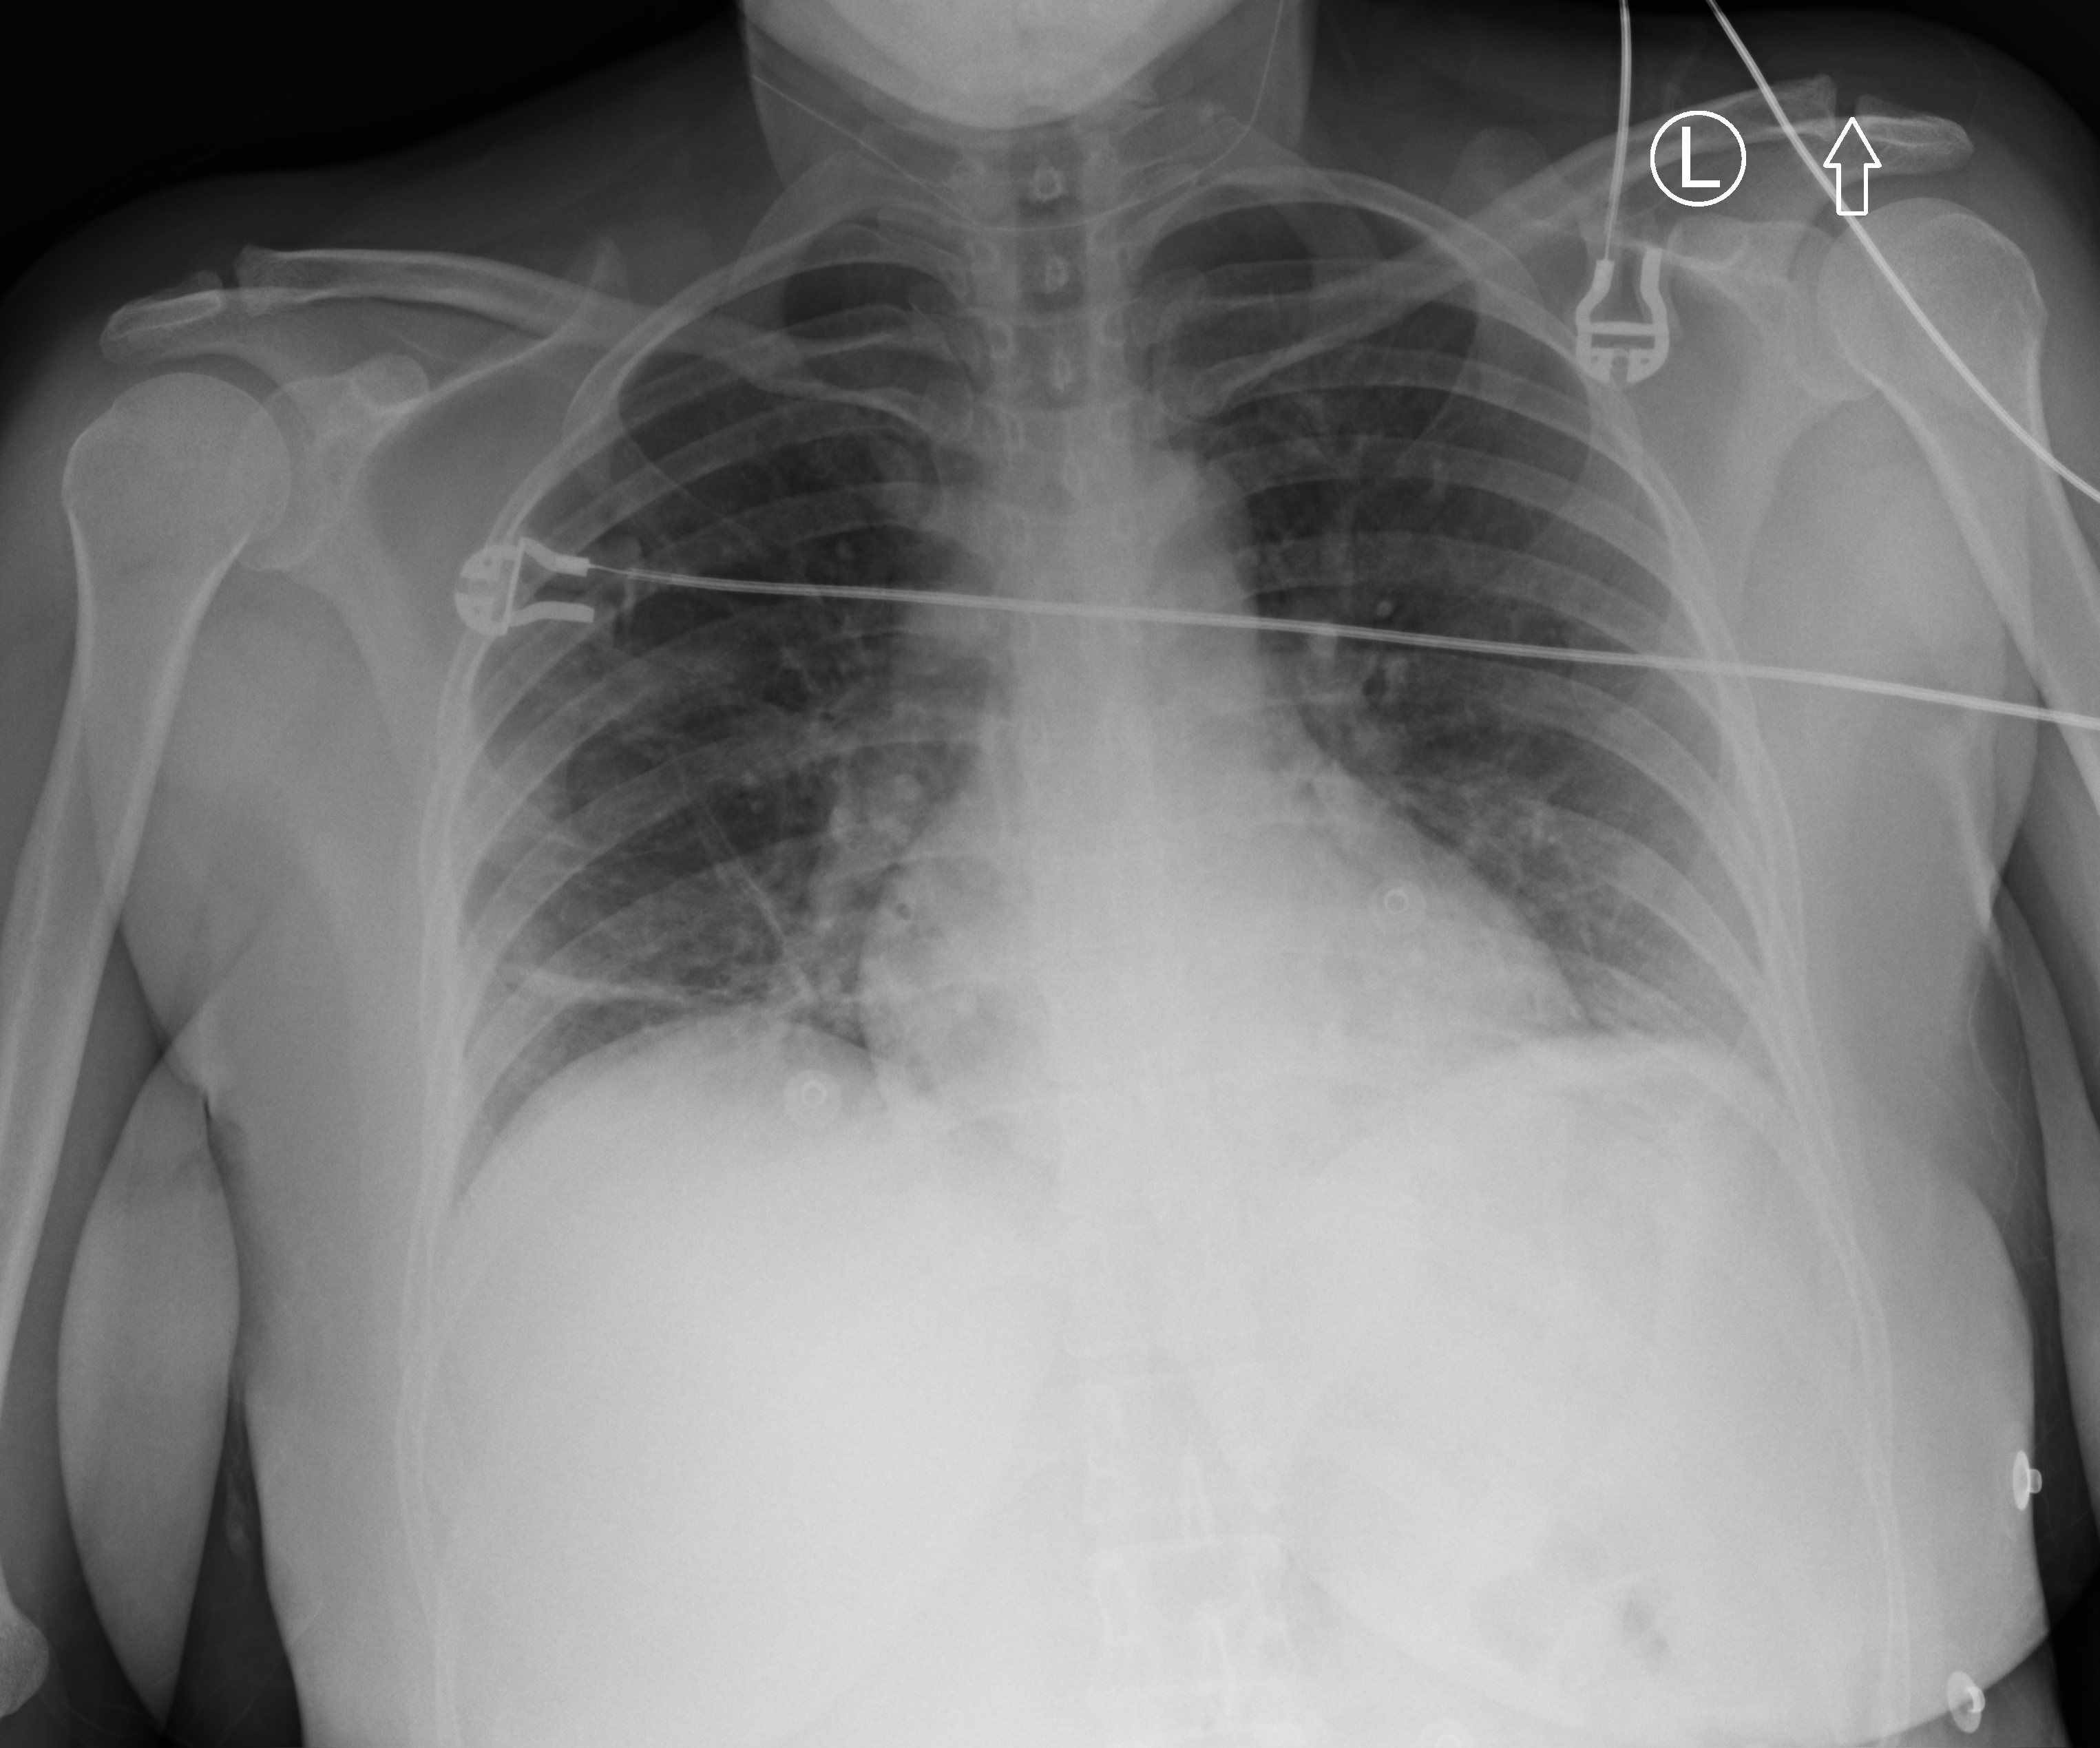
Portable chest radiograph. Female patient hospitalised with COVID-19, age 18–59 years.
Admission-level facts for this patient (not findings on this image; timing relative to this image not recorded): mechanically ventilated during this hospital stay: no; admitted to intensive care during this hospital stay: no.